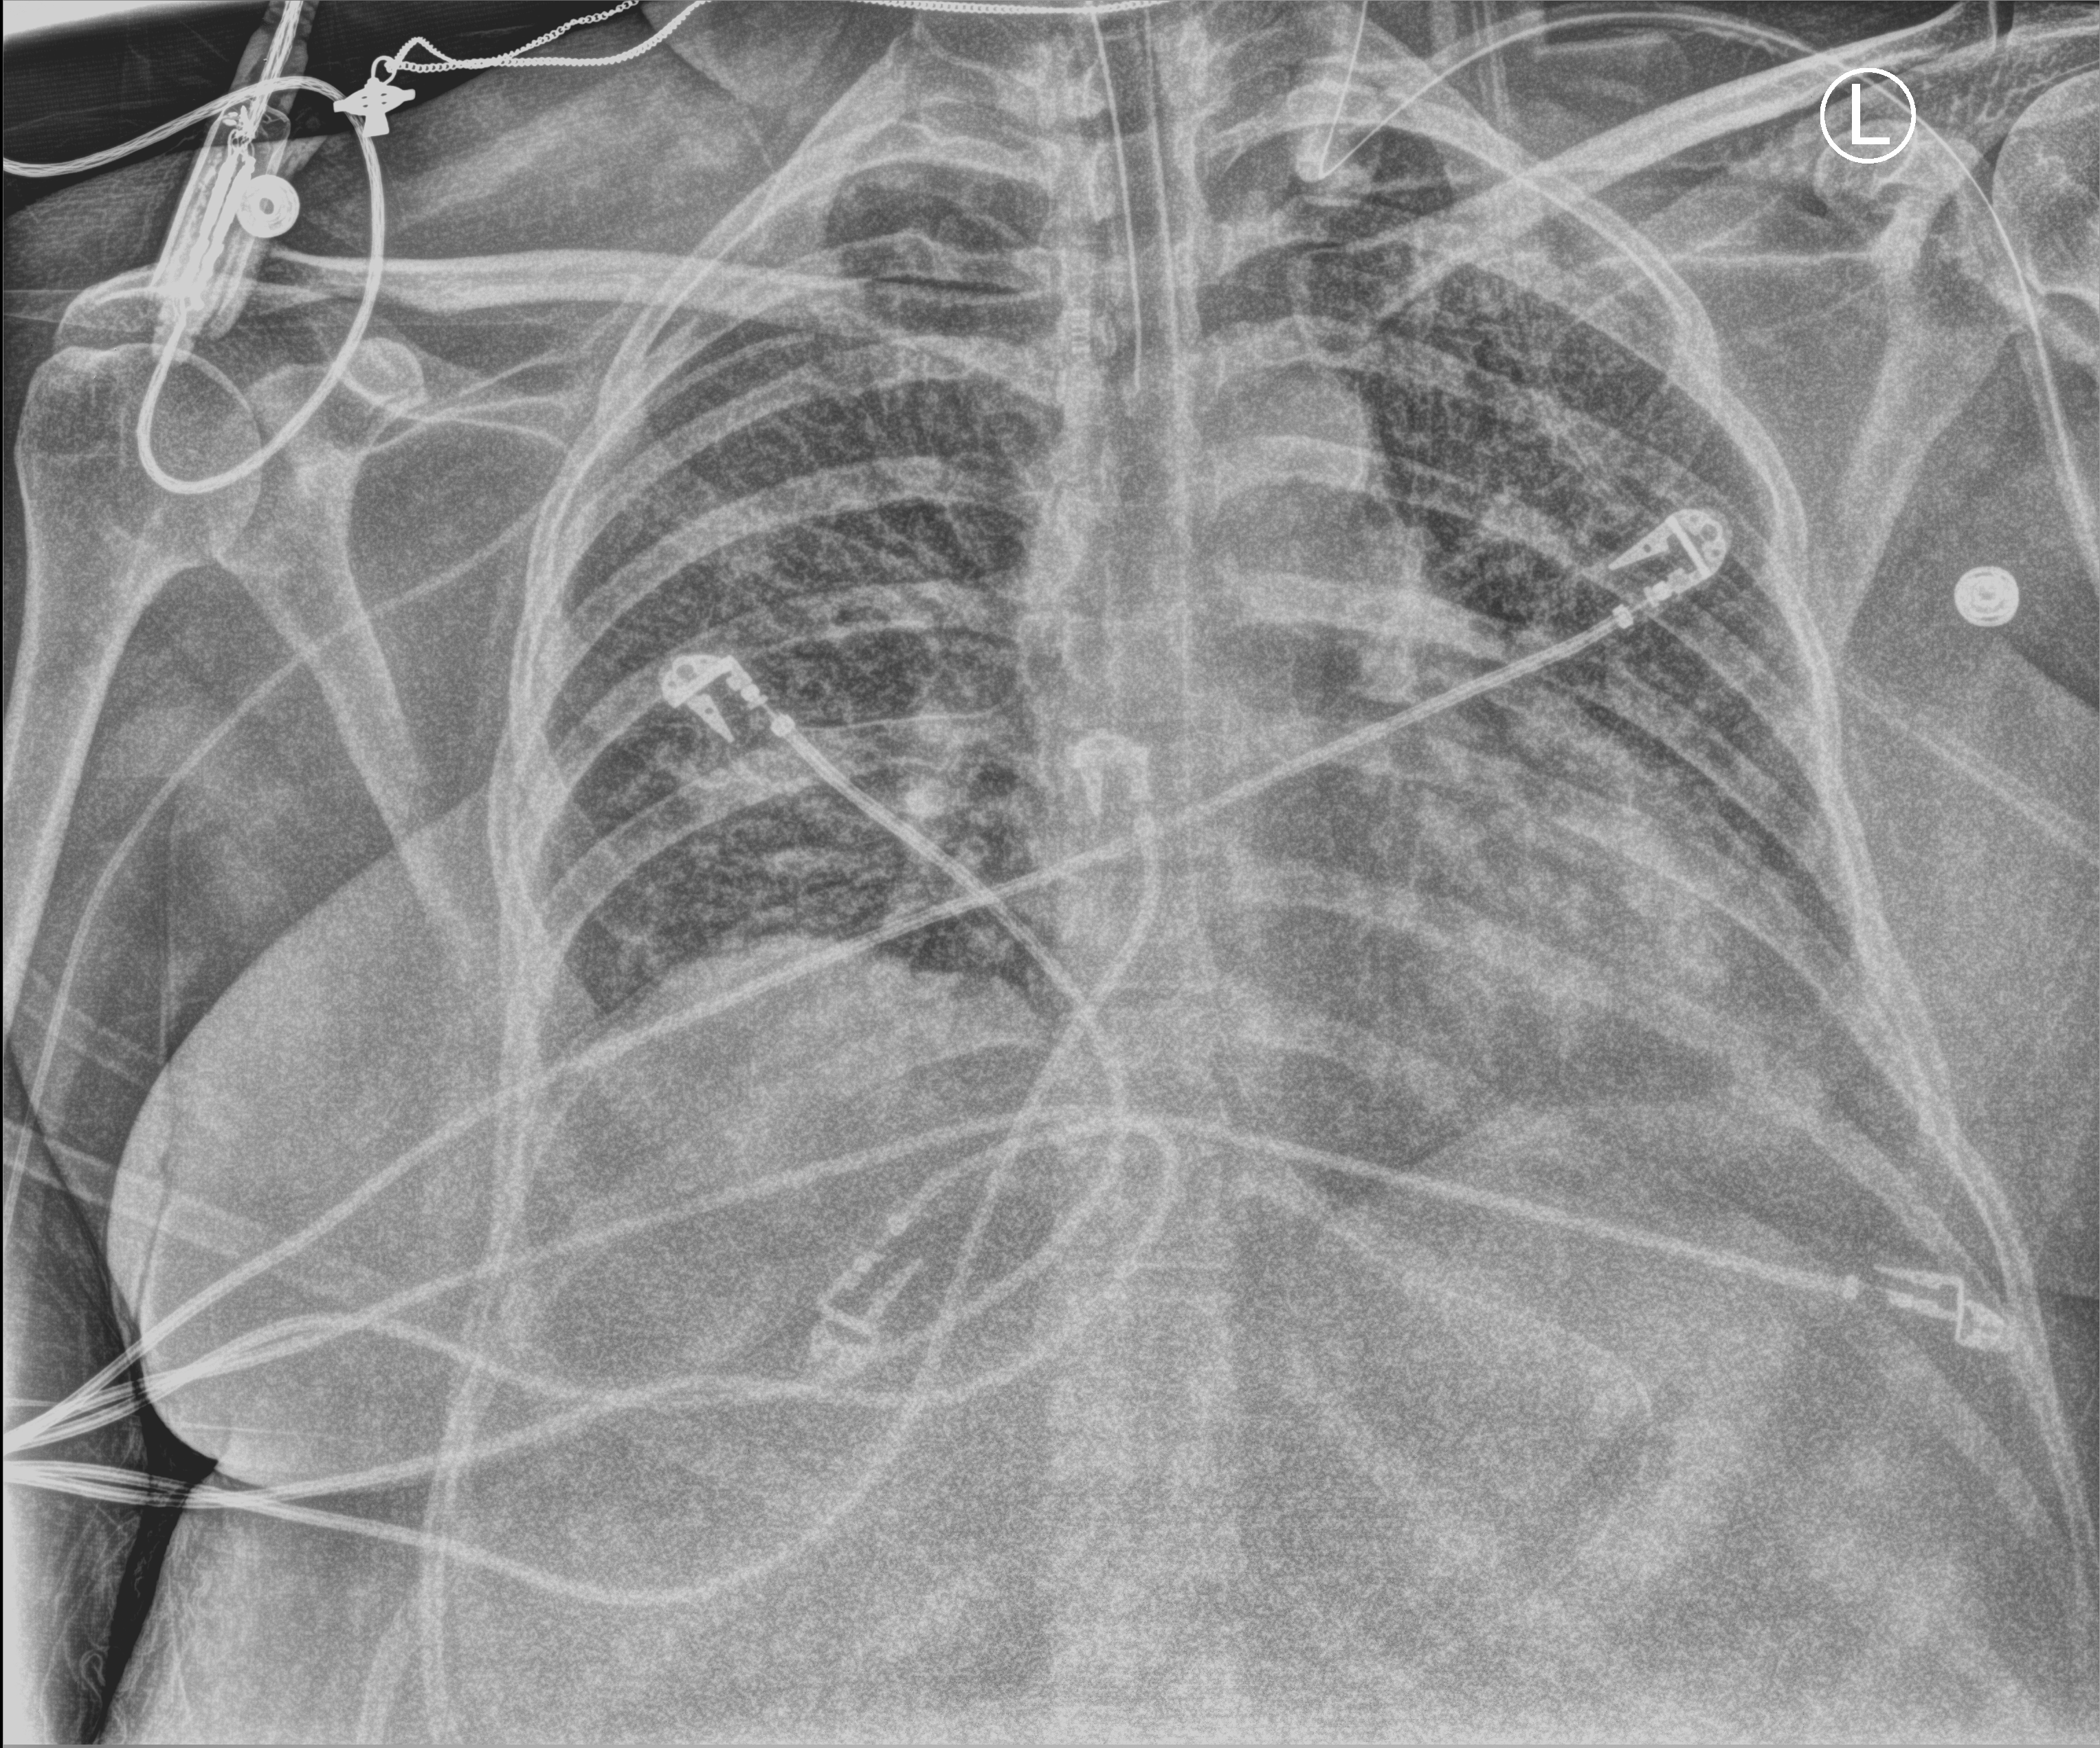
Portable chest radiograph. Female patient hospitalised with COVID-19, age 18–59 years.
From the hospital-stay record, not from the radiograph (when in the stay this image was taken is not recorded): admitted to intensive care during this hospital stay: yes; mechanically ventilated during this hospital stay: yes.